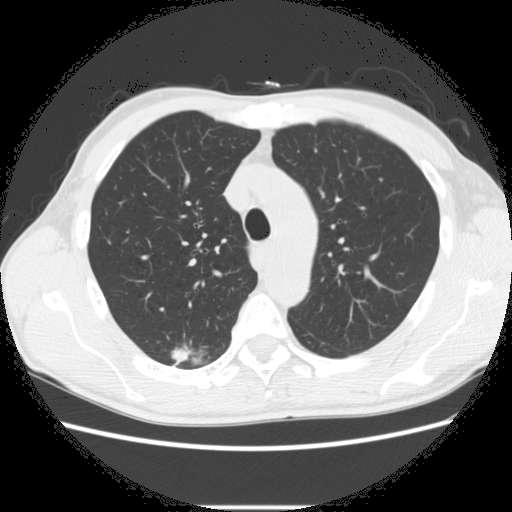
Low-dose screening chest CT, one axial slice. Position 207 of 282 along the scan axis. 120 kVp. Lung window (W 1500 / L -600 HU). 2.5 mm slice thickness. 512 × 512 image matrix.
Annotated regions visible in this slice (outlined manually by an expert reader):
- lesion 1 (tumor, upper lobe of right lung): bounding box [x1, y1, x2, y2] px = [171, 348, 189, 364]